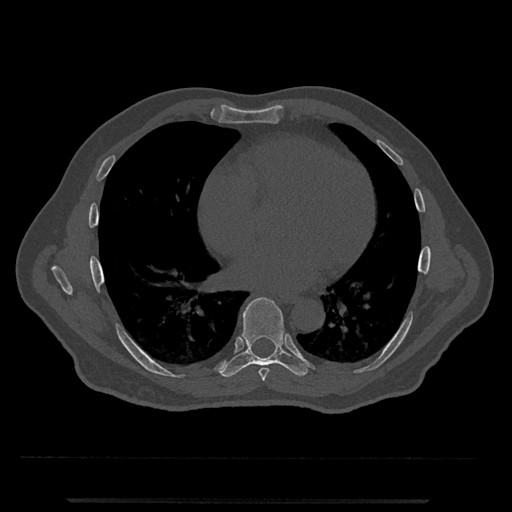
CT including the spine, one axial slice. Position 643 of 797 along the scan axis. 120 kVp. Bone window (W 1800 / L 400 HU). 0.5 mm slice thickness. 512 × 512 image matrix, field of view 419 × 419 mm. Male patient, age 63 years. From the clinical record (not read from this slice): primary cancer: prostate.
Outlined on this slice (semi-automatically segmented with operator editing):
- T7 vertebra: box from (x=259, y=368) to (x=269, y=381) px
- T8 vertebra: (x=220, y=297)–(x=314, y=377)